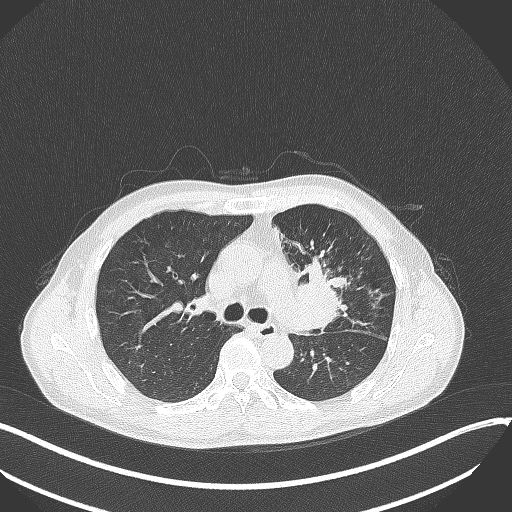
Chest CT, one axial slice. Slice 216 of 411 in the series (ordered by position). Lung window (W 1500 / L -600 HU). 512 × 512 image matrix, field of view 400 × 400 mm. Patient: male, 56 years. From the clinical record (not read from this slice): clinical TNM (as recorded): T2a N0 M0.
Structures marked on this image (bounding box drawn by a radiologist):
- lung tumour (recorded histology: squamous cell carcinoma): bounding box [x1, y1, x2, y2] px = [290, 258, 348, 342]